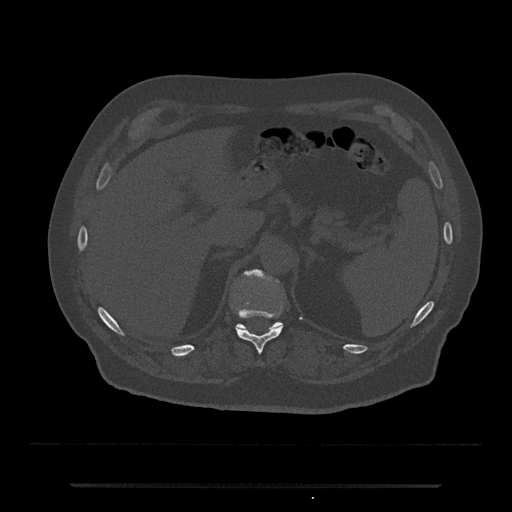
CT including the spine, one axial slice; slice 635 of 797 in the series (ordered by position); 120 kVp; bone window (W 1800 / L 400 HU); 0.5 mm slice thickness; 512 × 512 image matrix, field of view 434 × 434 mm. Male patient, age 80 years. From the clinical record (not read from this slice): primary cancer: prostate.
Outlined on this slice (semi-automatically segmented with operator editing):
- T11 vertebra: bounding box [x1, y1, x2, y2] px = [236, 309, 283, 364]
- T12 vertebra: [236, 269, 283, 331]